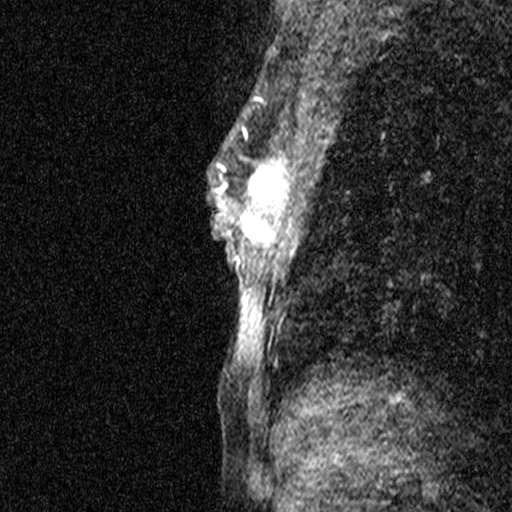
Breast MRI (dynamic contrast-enhanced), one sagittal slice. Position 25 of 44 along the scan axis. Dynamic contrast-enhanced study with each time point stored as its own series, time point 2 of 3 at this slice position (early post-contrast, ordered by acquisition time). 1.5 T. TE 4.5 ms, TR 11 ms. 3 mm slice thickness. 512 × 512 image matrix. Female patient, age 44 years. Case-level facts recorded for this patient, not image findings: setting: breast cancer imaged before/during neoadjuvant chemotherapy; receptor status: HR-positive, HER2-negative.
Structures marked on this image (semi-automatically segmented with operator editing):
- analysis volume of interest (the breast-tissue region the enhancement analysis was run in; not a lesion): bounding box [x1, y1, x2, y2] px = [218, 118, 282, 291]
- tumour enhancement mask (voxels above the 90 % enhancement threshold inside the analysis volume of interest): [218, 127, 282, 242]